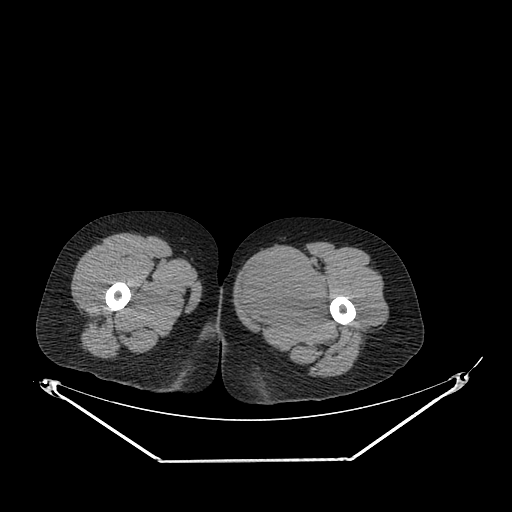
CT of an extremity soft-tissue mass (from a PET/CT study), one axial slice. Slice 242 of 267 in the series (ordered by position). Reconstruction kernel SOFT. 120 kVp. Soft-tissue window (W 400 / L 40 HU). 3.75 mm slice thickness. 512 × 512 image matrix, field of view 500 × 500 mm. Female patient. Case-level facts recorded for this patient, not image findings: histological type: pleiomorphic leiomyosarcoma; grade: intermediate; site of the primary tumour: left thigh.
Structures marked on this image (expert contour drawn on MRI and transferred to this co-registered scan by the dataset authors):
- gross tumour volume including surrounding oedema: bounding box (x1, y1, x2, y2) in pixels: (237, 258, 328, 330)
- gross tumour volume (mass): (237, 260, 327, 328)